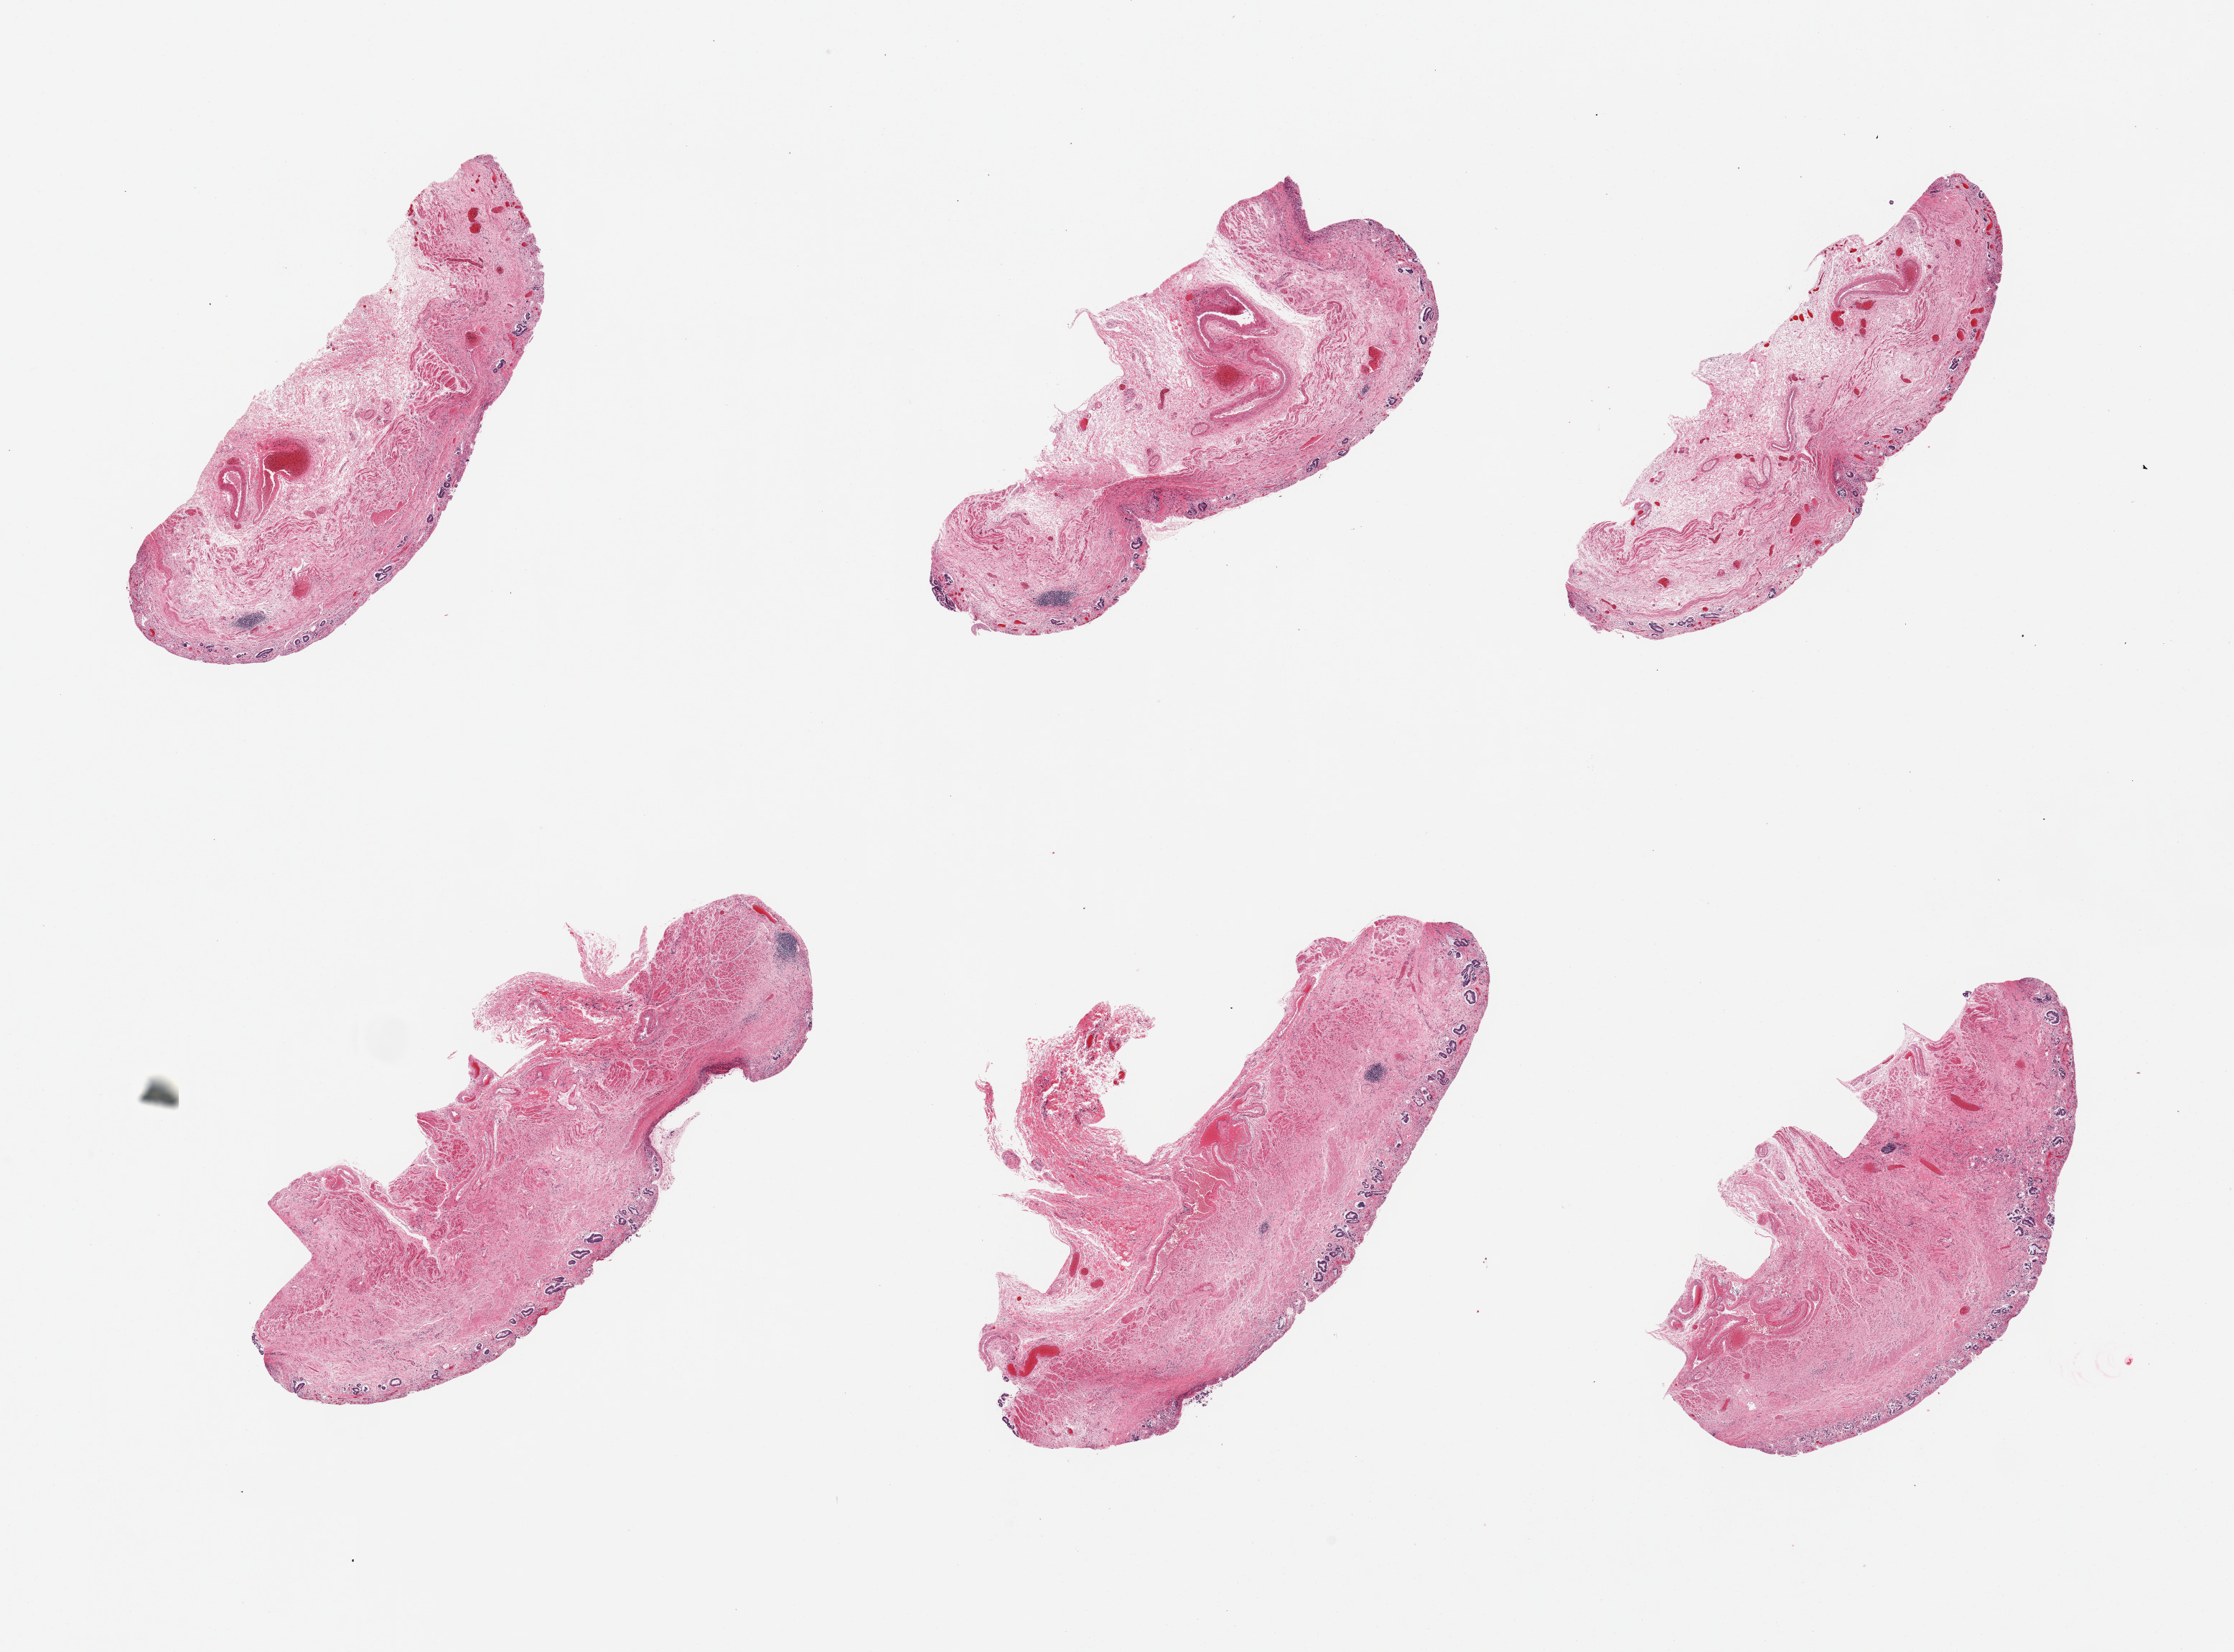
Whole-slide image, H&E stain, brightfield, whole scanned area (about 24.6 x 18.2 mm) shown as a low-resolution overview, PAXgene-fixed paraffin-embedded (PFPE) section, section of esophageal mucous membrane (target tissue), donor tissue sample. Male donor.
Review note (as recorded): 6 pieces; largely sloughed glandular mucosa consistent with Barrett esophagus (clinical history).